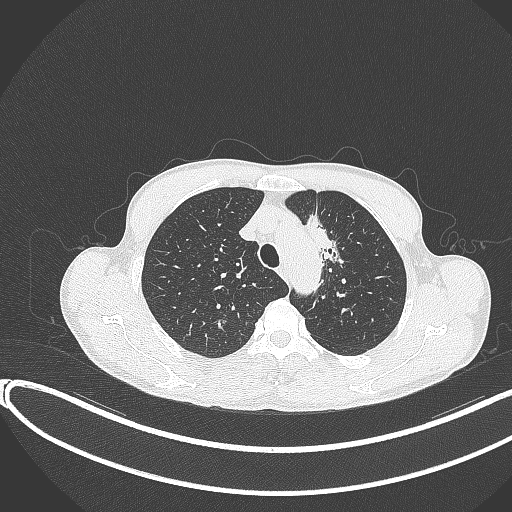
Chest CT, one axial slice; reconstruction kernel B70f; lung window (W 1500 / L -600 HU); 512 × 512 image matrix. Patient: male, 58 years. Case-level facts recorded for this patient, not image findings: clinical TNM (as recorded): T1c N1 M0.
Outlined on this slice (rectangle marked by the reading radiologist):
- lung tumour (recorded histology: adenocarcinoma): bounding box [x1, y1, x2, y2] px = [304, 206, 350, 271]